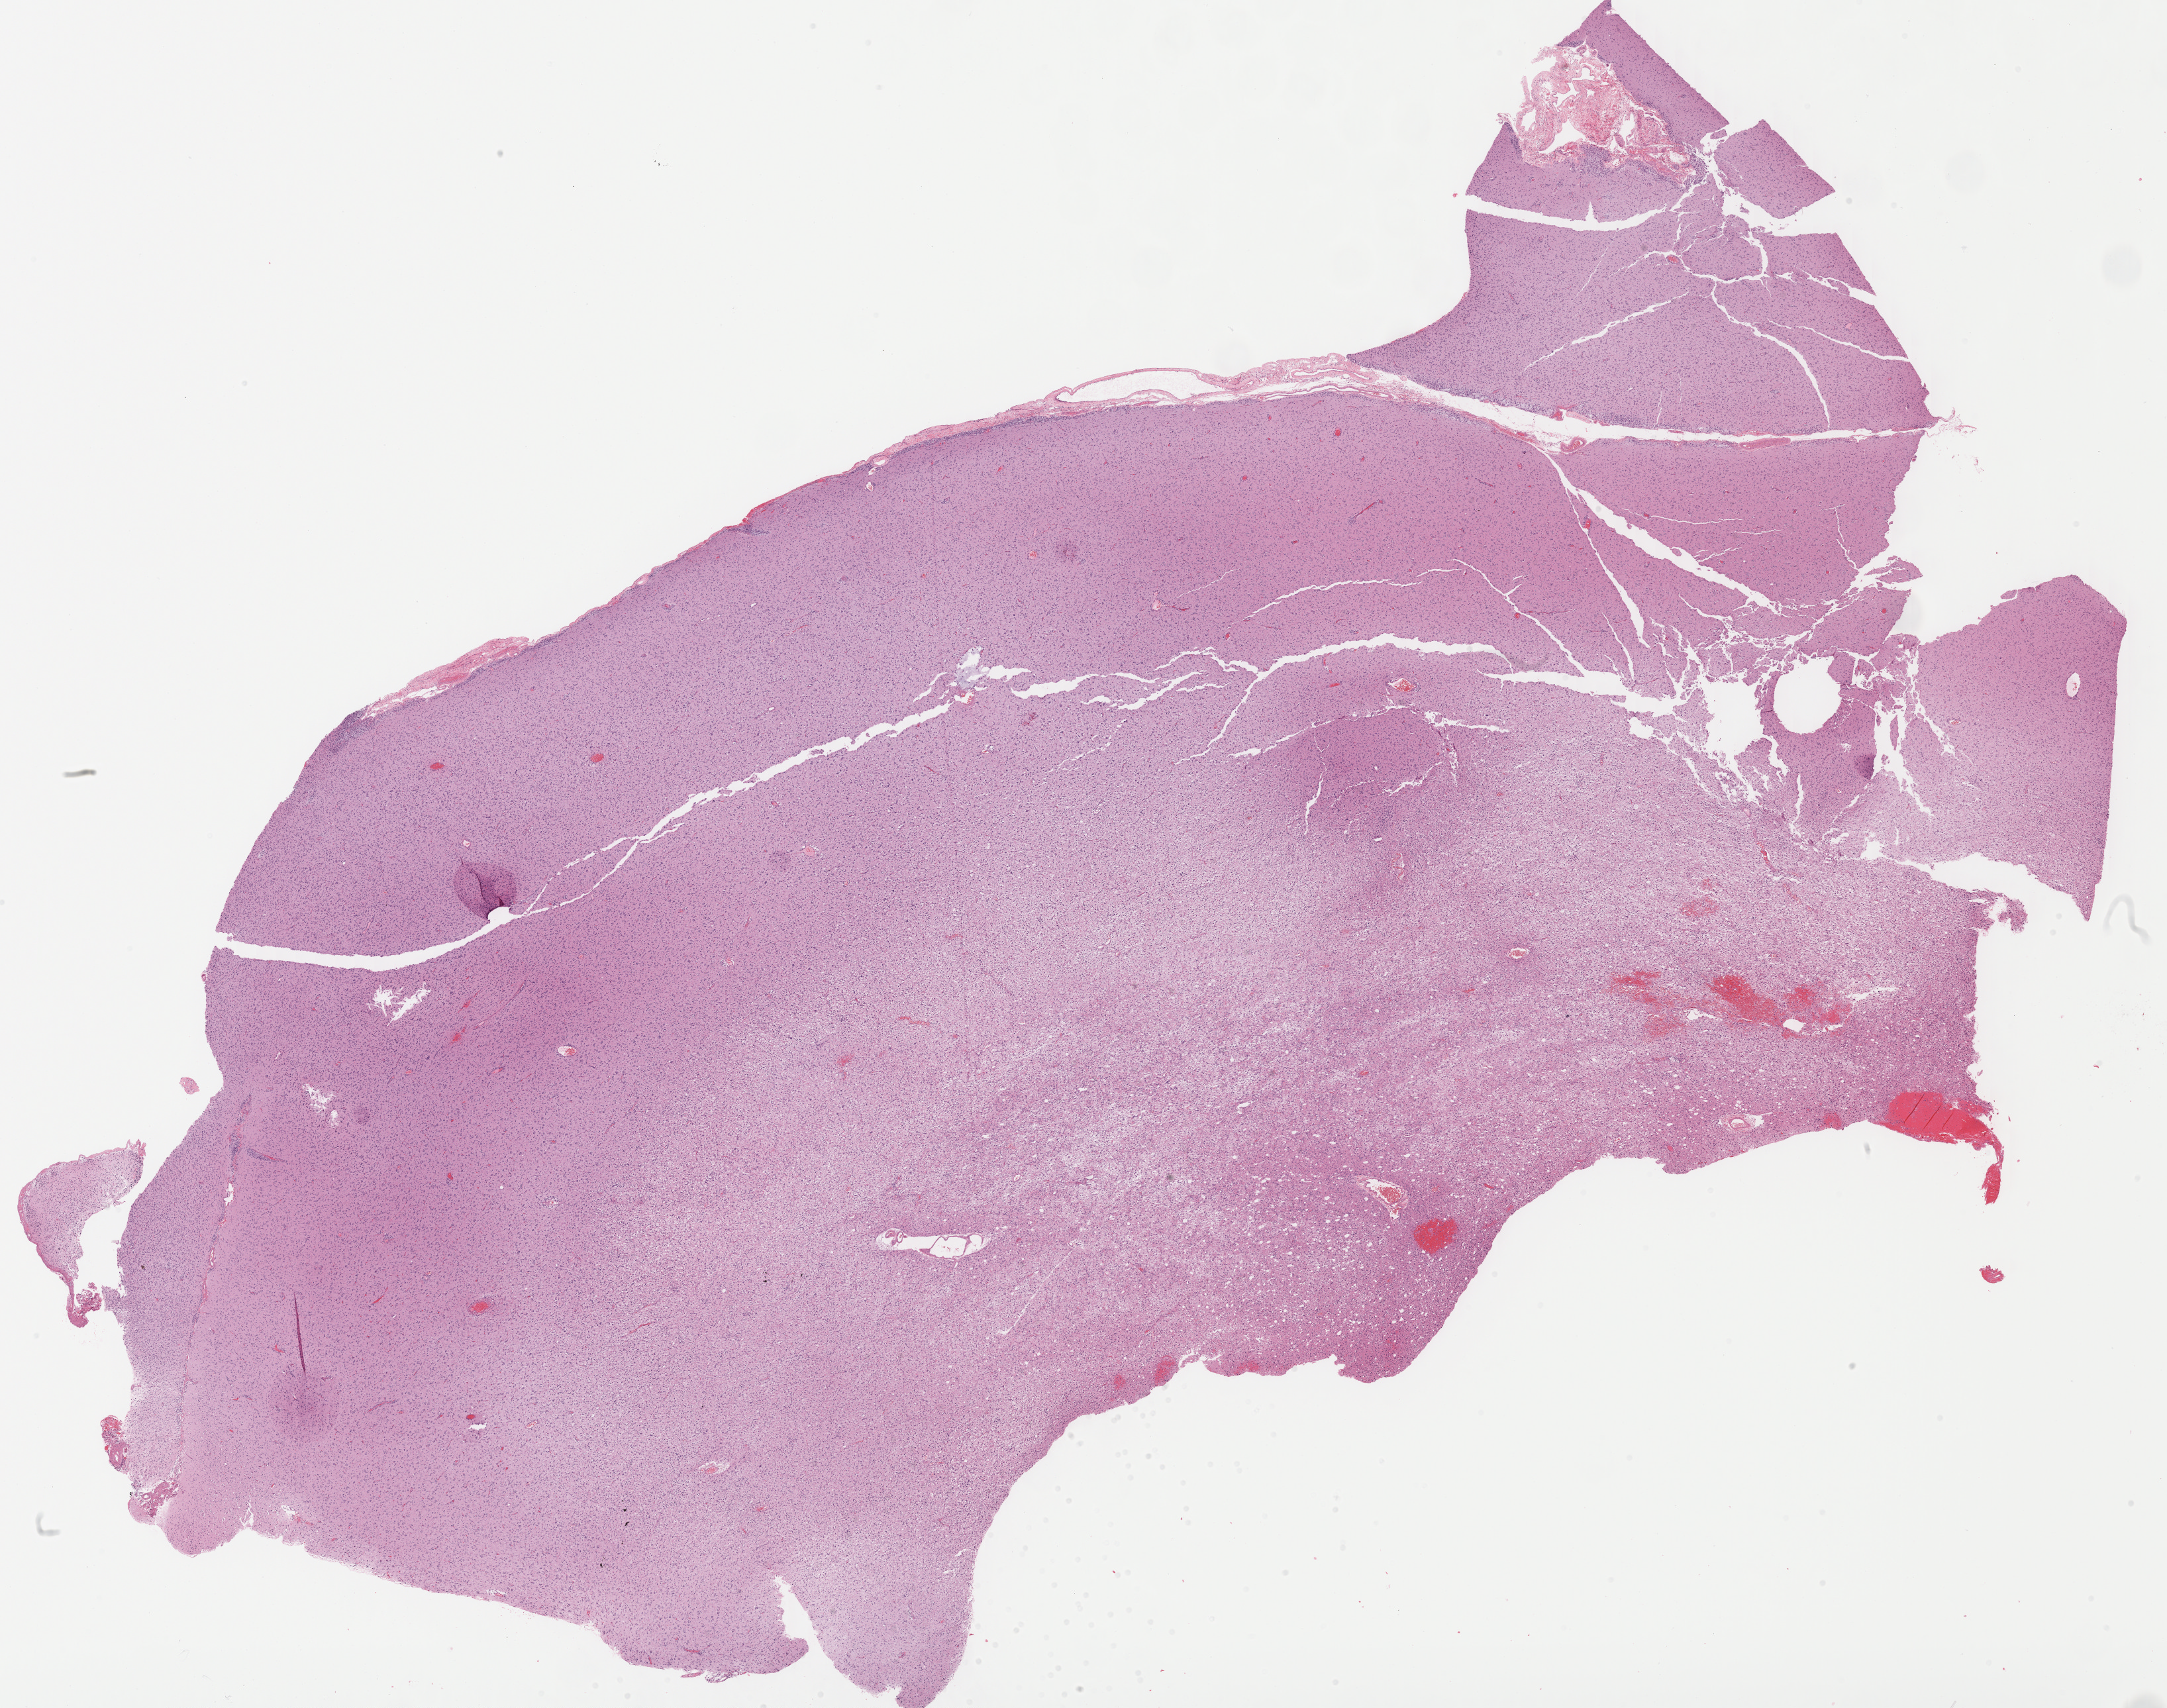
Digitized H&E-stained tissue section (whole slide), a low-resolution overview of the entire scanned area, about 25.8 x 20.3 mm, formalin-fixed paraffin-embedded (FFPE) diagnostic section, primary tumour sample from the brain. Patient: male, age at initial diagnosis 34 years. Histologic grade: G3 (poorly differentiated).
• diagnosis: Astrocytoma, anaplastic (cerebrum)